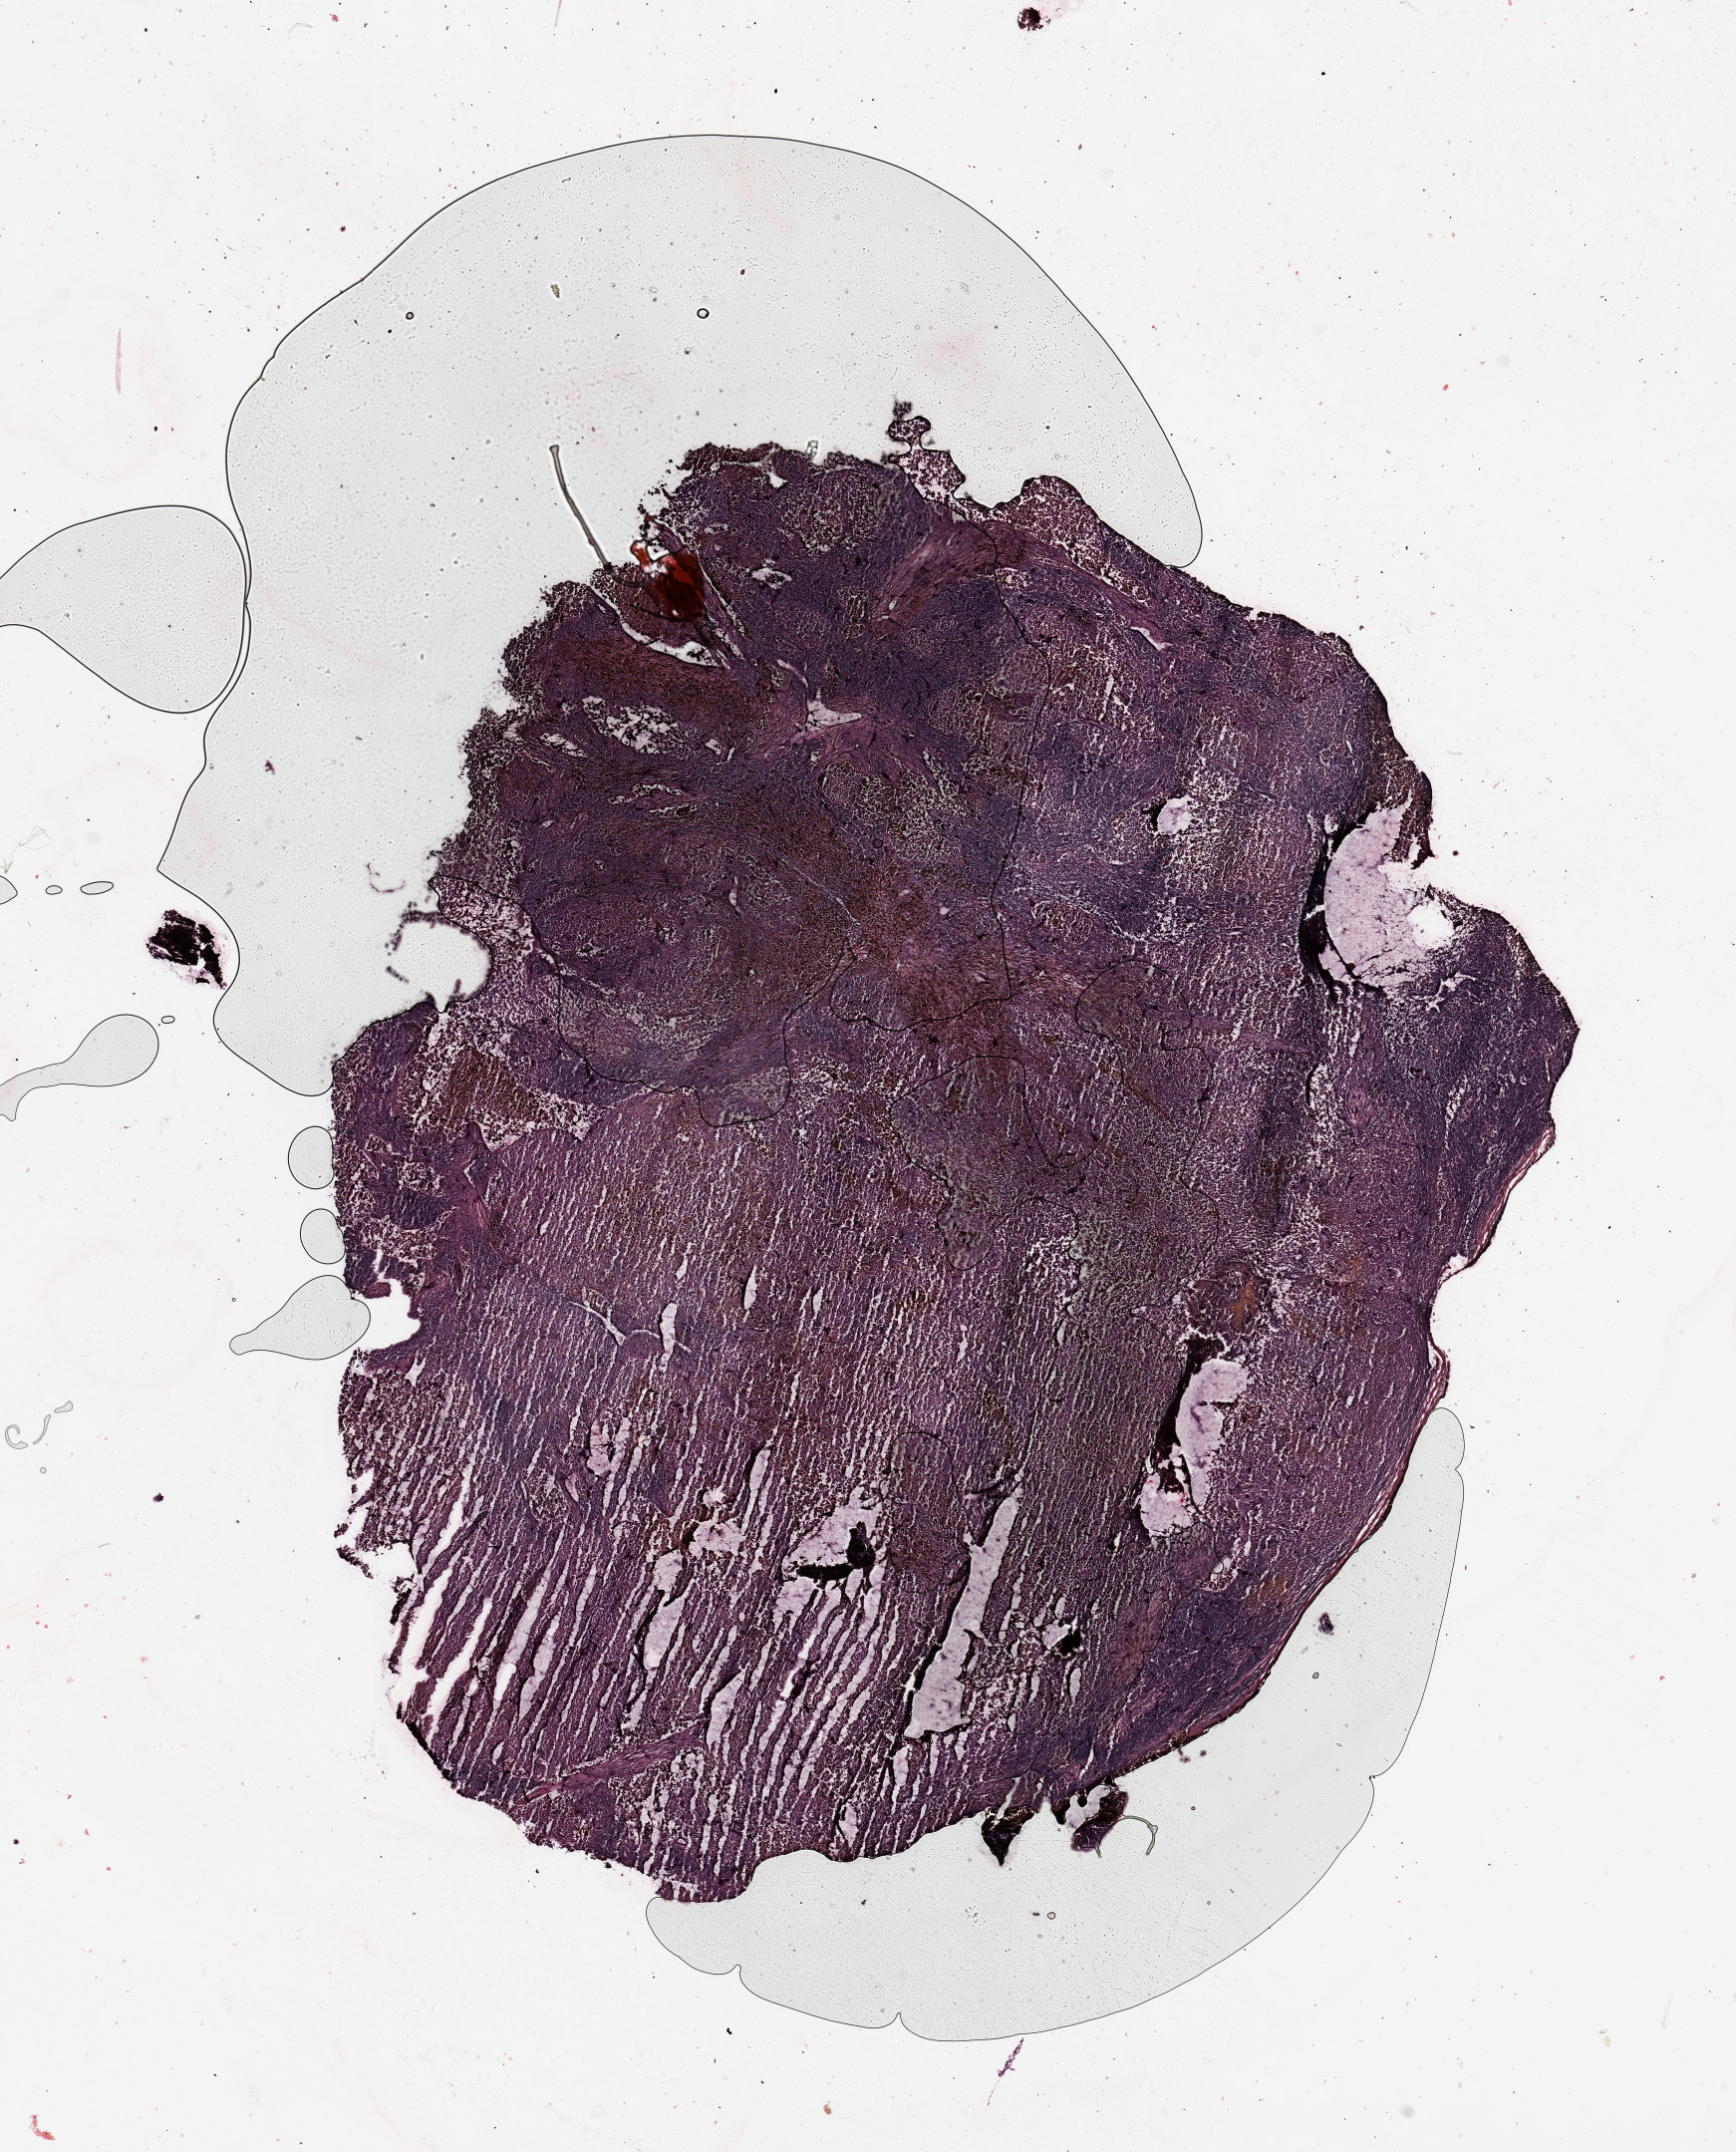
Whole-slide histology image, Hematoxylin and eosin (H&E) stained — low-resolution overview of the scanned area, about 13.8 x 17.1 mm; melanoma tumour tissue; sampled site not recorded. 23-year-old female patient.
Patient diagnosis (cohort enrolment): cutaneous melanoma (skin).